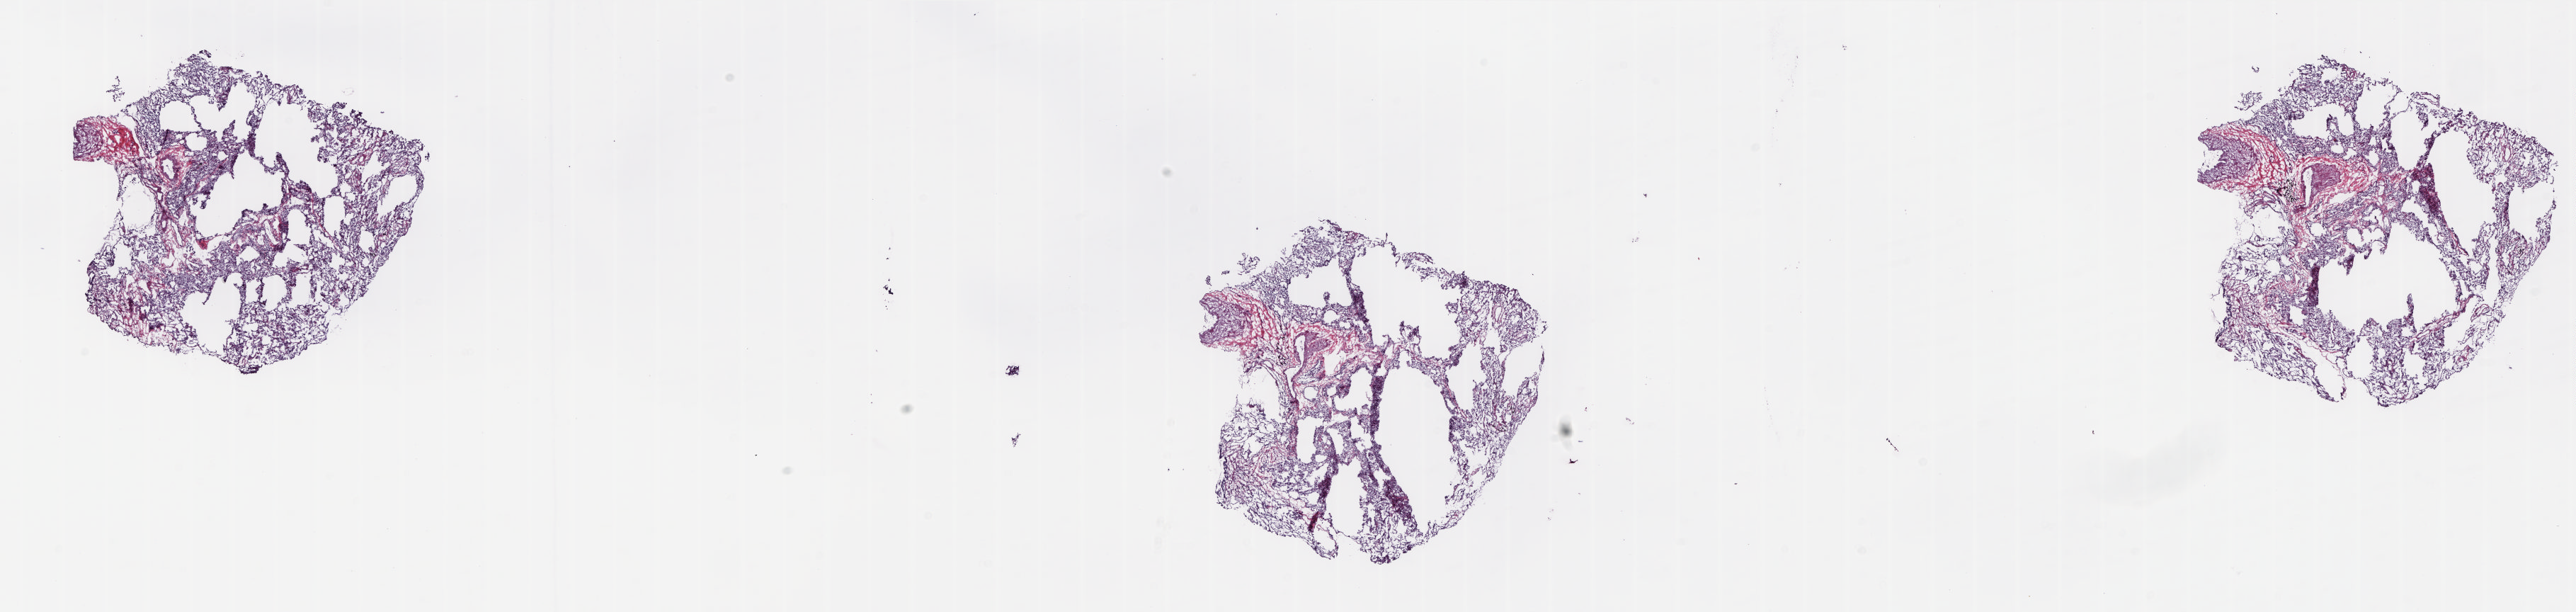
Whole-slide histology image, Hematoxylin and eosin (H&E) stained — whole scanned area (about 29.3 x 7.0 mm) shown as a low-resolution overview, frozen section, lung, solid tissue normal (non-tumour tissue) sample. Patient: male, age at initial diagnosis 59 years. Slide review estimates, as recorded: tumour cells 0%, tumour nuclei 0%, normal cells 100%, stromal cells 0%, necrosis 0%. Inflammatory infiltration, as recorded: lymphocyte infiltration 5%, monocyte infiltration 7%, neutrophil infiltration 0%.
• this section: solid tissue normal (non-tumour) sample from the same patient
• patient diagnosis: Adenocarcinoma, NOS (upper lobe, lung)